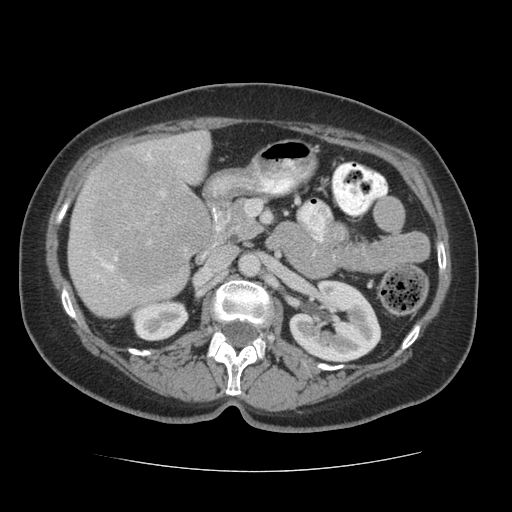
Contrast-enhanced abdominal CT (liver protocol), one axial slice. Slice 23 of 75 in the series (ordered by position). Reconstruction kernel STANDARD. 140 kVp. Soft-tissue window (W 400 / L 40 HU). 2.5 mm slice thickness. 512 × 512 image matrix, field of view 360 × 360 mm. Case-level facts recorded for this patient, not image findings: diagnosis: hepatocellular carcinoma (patient treated with transarterial chemoembolisation; whether this scan precedes or follows treatment is not stated here); TNM stage (as recorded): Stage-I; Child-Pugh class: A.
Annotated regions visible in this slice (semi-automatic segmentation, software-assisted and operator-edited):
- liver parenchyma outside the tumour (the mass and vessels are separate outlines, so this box may not span the whole liver): bounding box (x1, y1, x2, y2) in pixels: (68, 130, 210, 318)
- mass: (76, 151, 211, 295)
- liver vessels: (97, 145, 201, 278)